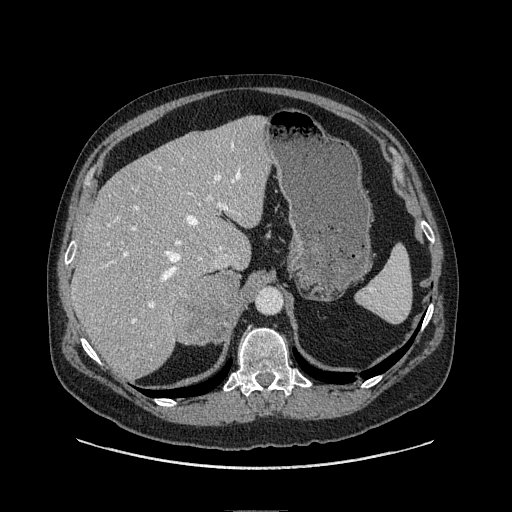
Contrast-enhanced abdominal CT, one axial slice; soft-tissue window (W 400 / L 40 HU); 1.25 mm slice thickness; 512 × 512 image matrix. Male patient. Case-level facts recorded for this patient, not image findings: diagnosis: adrenocortical carcinoma; tumour side: right adrenal; tumour size at pathology: 7.5 cm; Ki-67 index: 15 %; stage (as recorded): 2.
Annotated regions visible in this slice (semi-automatically segmented with operator editing):
- mass: box from (x=177, y=274) to (x=241, y=346) px